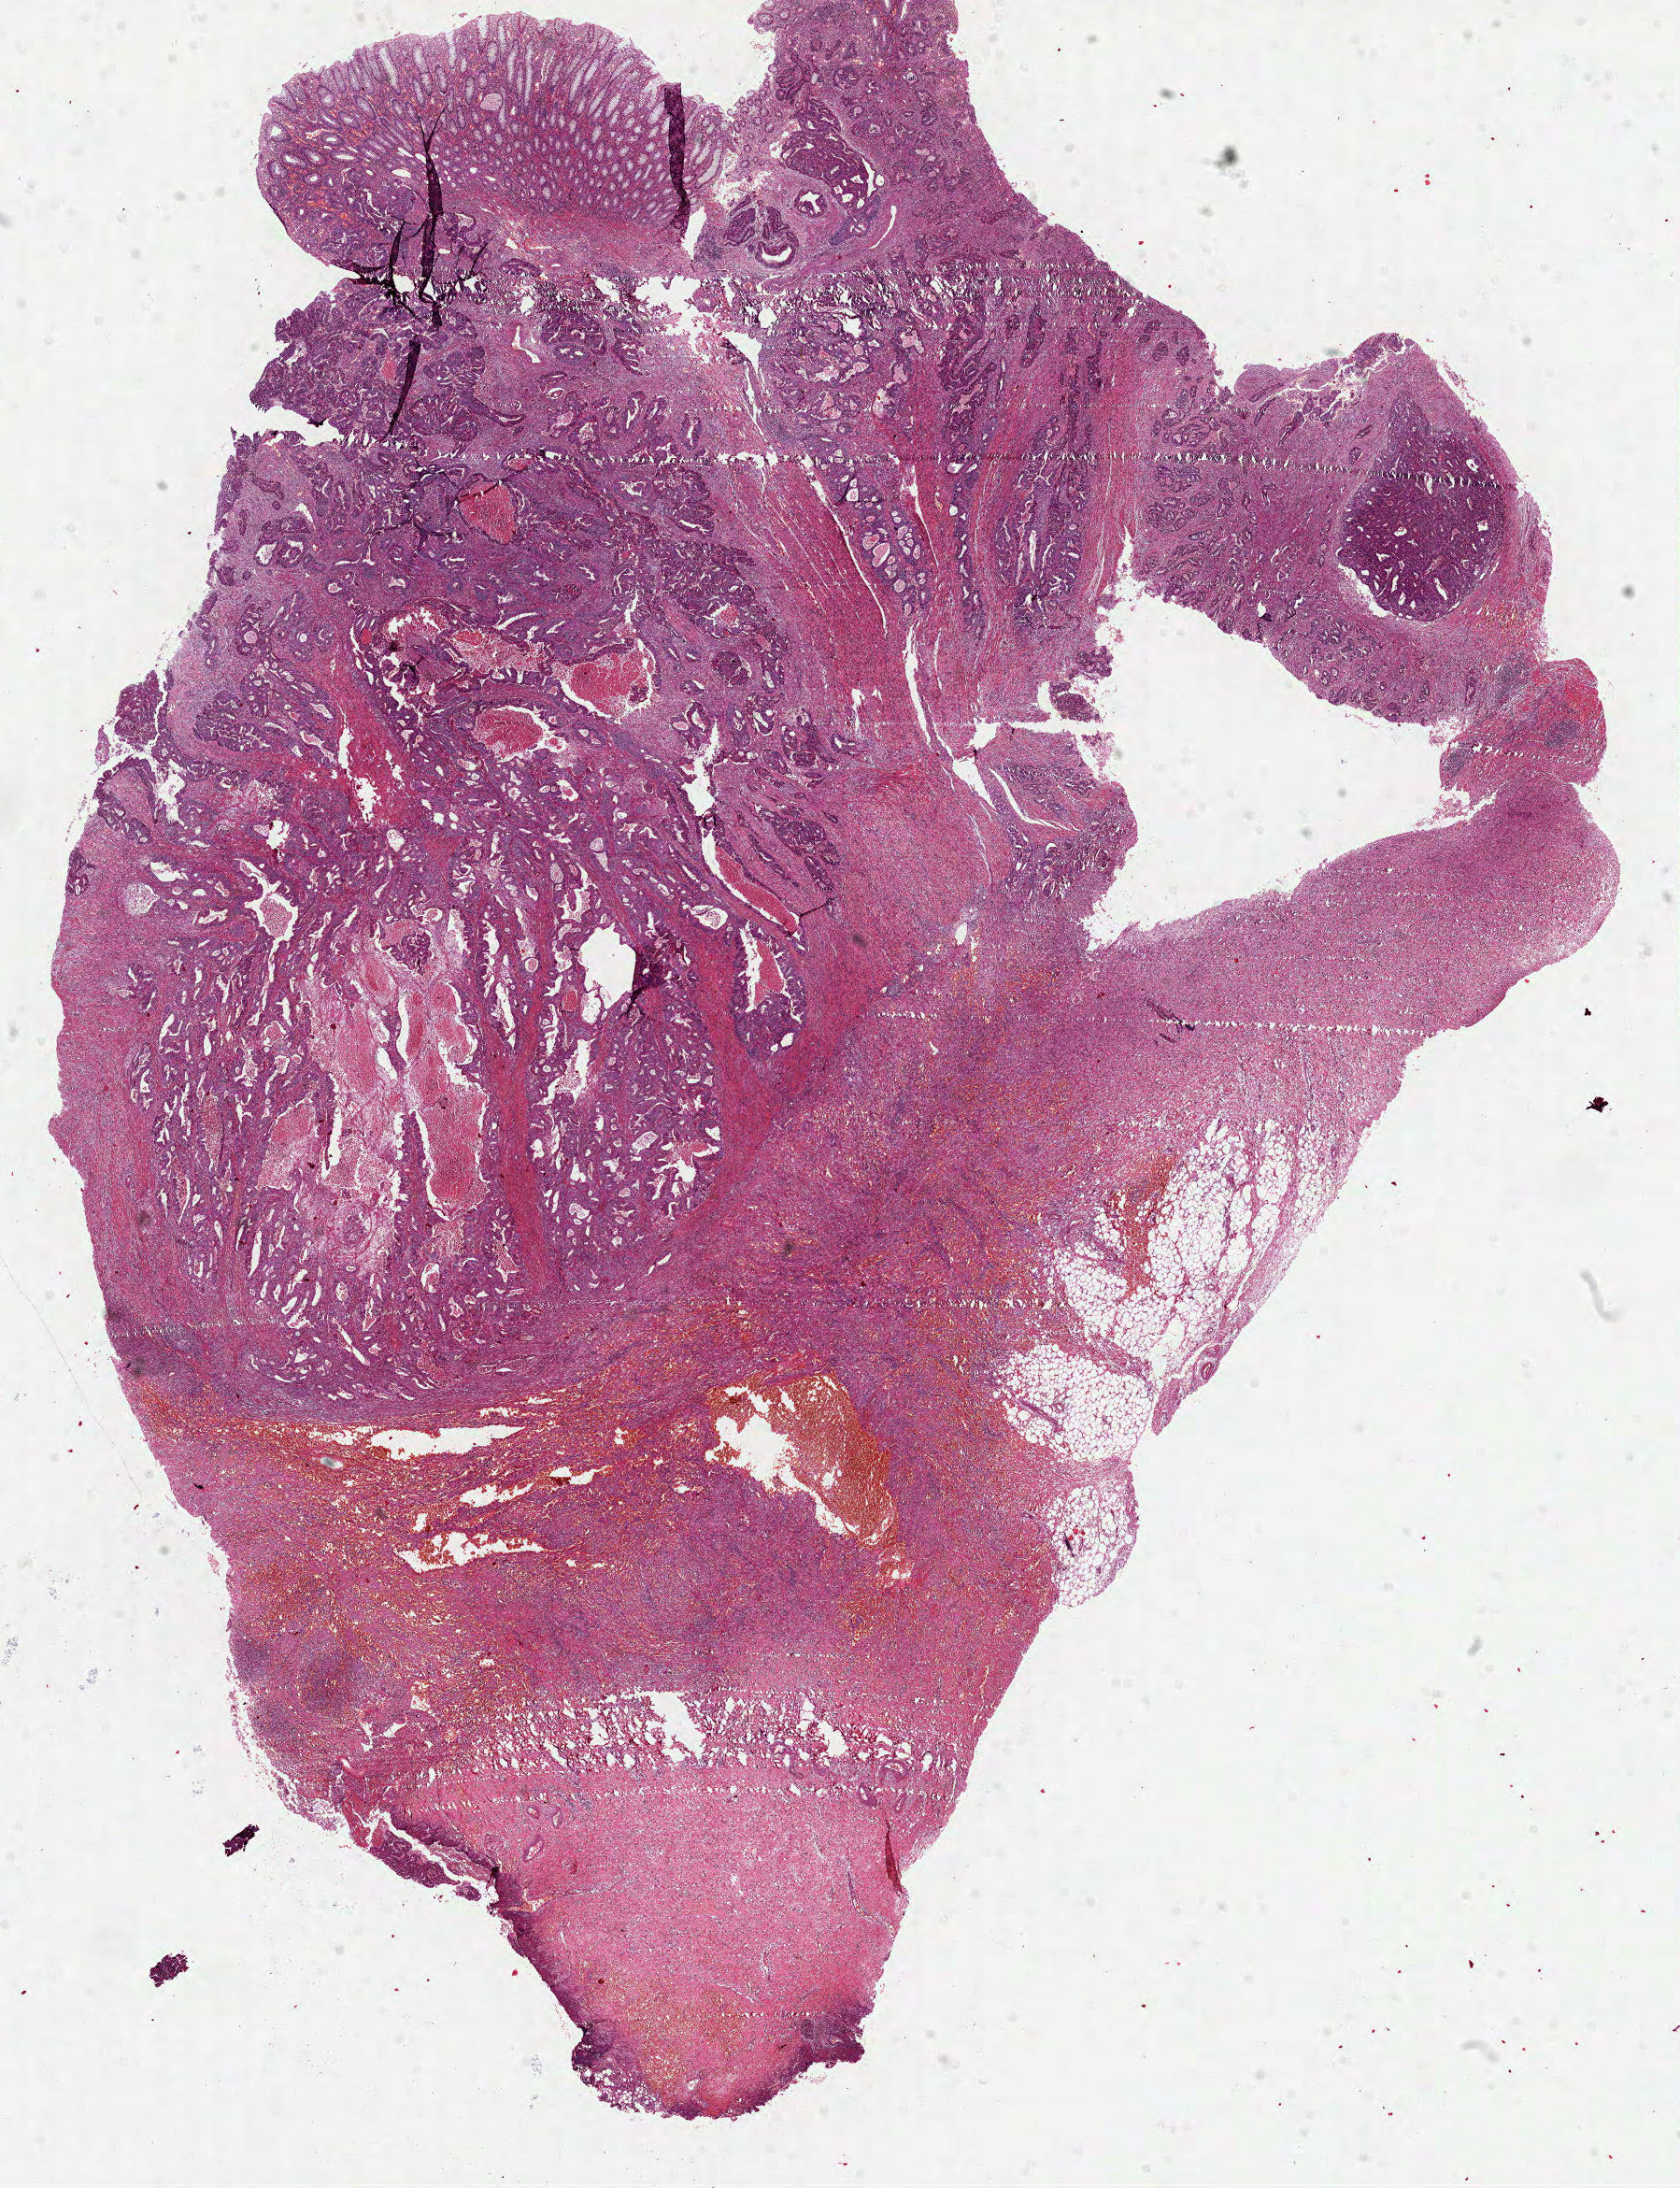
Hematoxylin and eosin (H&E) stained whole-slide image, whole scanned area (about 14.5 x 18.9 mm) shown as a low-resolution overview. Formalin-fixed paraffin-embedded (FFPE) diagnostic section. Colon, primary tumour sample. Male, age 77 years at initial diagnosis.
* TNM: T3 N0 M0
* AJCC pathologic stage: IIA (6th edition)
* diagnosis: Adenocarcinoma, NOS